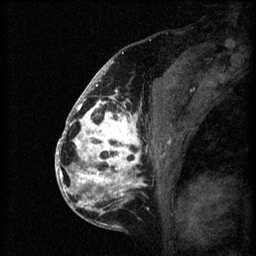
Breast MRI (dynamic contrast-enhanced), one sagittal slice. Position 32 of 60 along the scan axis. 3 images stored at this slice position (order not interpretable as contrast timing). 1.5 T. TE 4.2 ms, TR 8.2 ms. 256 × 256 image matrix, field of view 180 × 180 mm. Patient: female, 41 years.
Outlined on this slice (semi-automatically segmented with operator editing):
- analysis volume of interest (the breast-tissue region the enhancement analysis was run in; not a lesion): bounding box (x1, y1, x2, y2) in pixels: (72, 108, 170, 205)
- tumour enhancement mask (voxels above the 70 % enhancement threshold inside the analysis volume of interest): (72, 108, 170, 205)